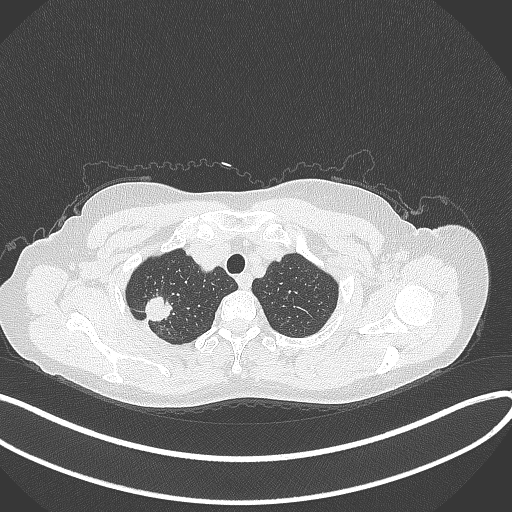
Chest CT, one axial slice; position 318 of 337 along the scan axis; 120 kVp; lung window (W 1500 / L -600 HU); 1 mm slice thickness; 512 × 512 image matrix, field of view 400 × 400 mm. Patient: female, 50 years. Case-level facts recorded for this patient, not image findings: clinical TNM (as recorded): T1c N0 M0.
Annotated regions visible in this slice (rectangle marked by the reading radiologist):
- lung tumour (recorded histology: adenocarcinoma): bounding box <140,293,177,323> (left, top, right, bottom; pixels)